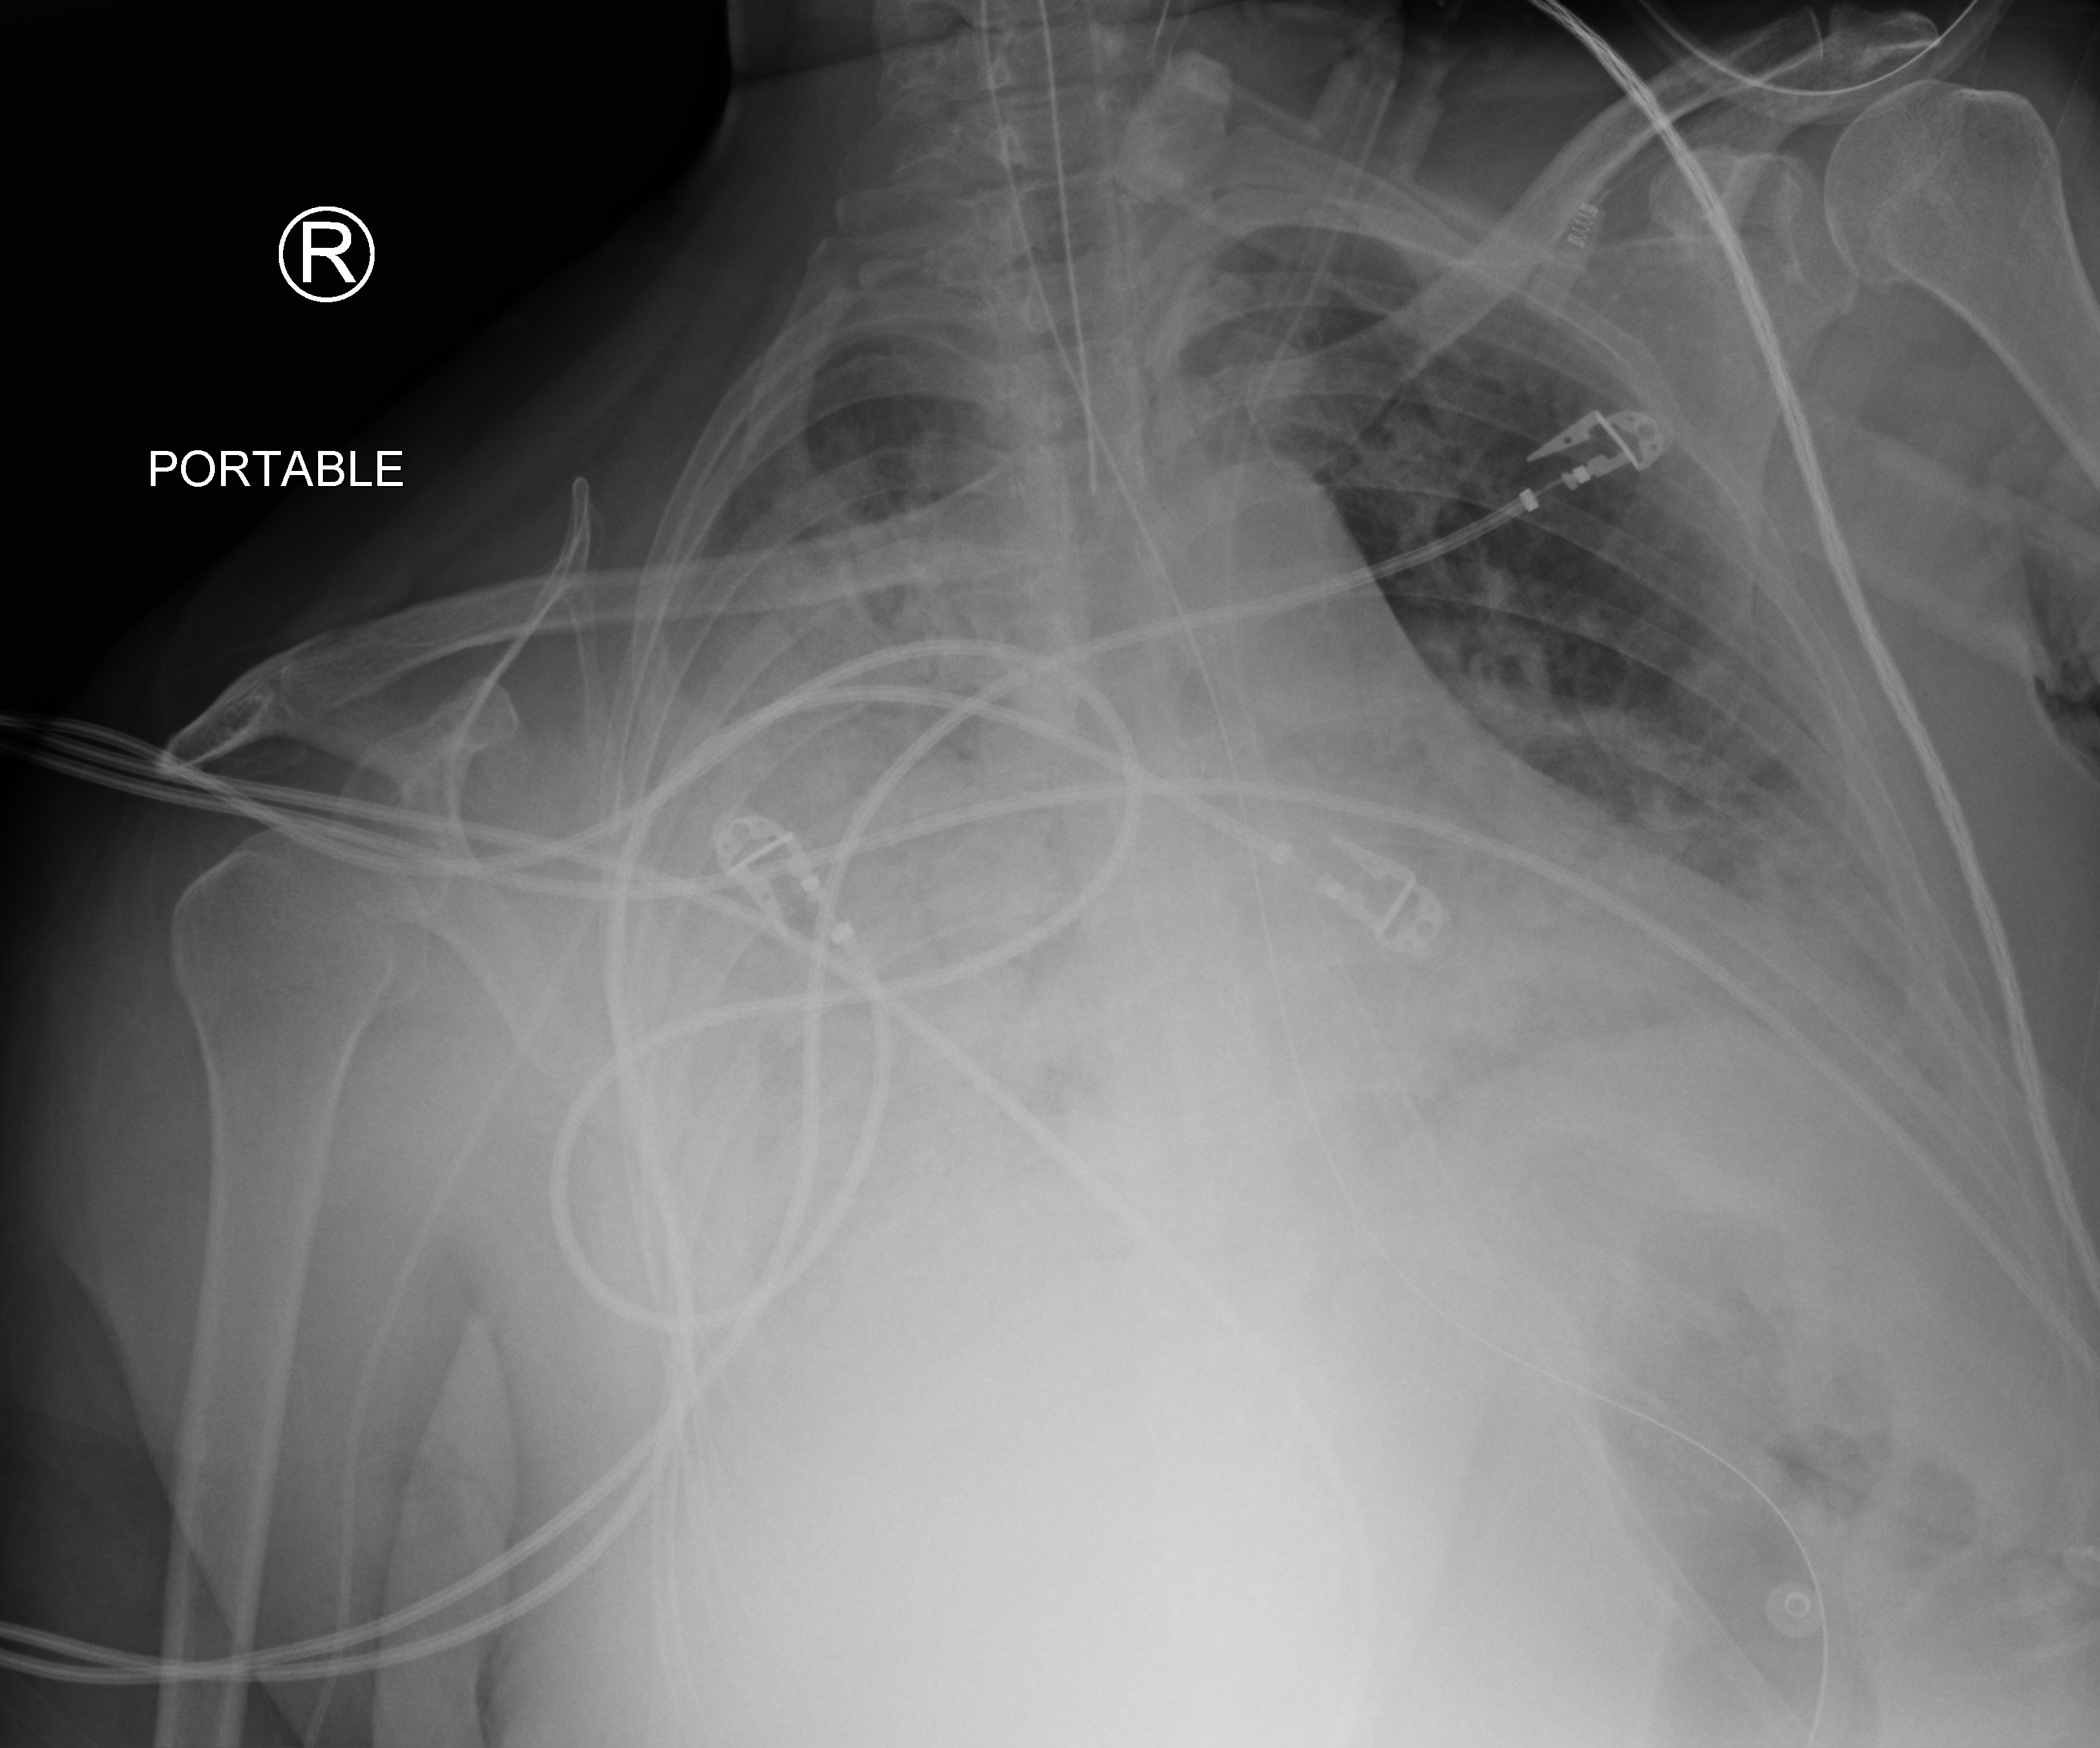
Bedside chest radiograph (computed radiography), anteroposterior (AP) projection. Female patient hospitalised with COVID-19, age 18–59 years.
Hospital-stay facts (about this admission, not read from this image; timing relative to this image not recorded): chronic kidney disease (admission record): no; hypertension (admission record): no.